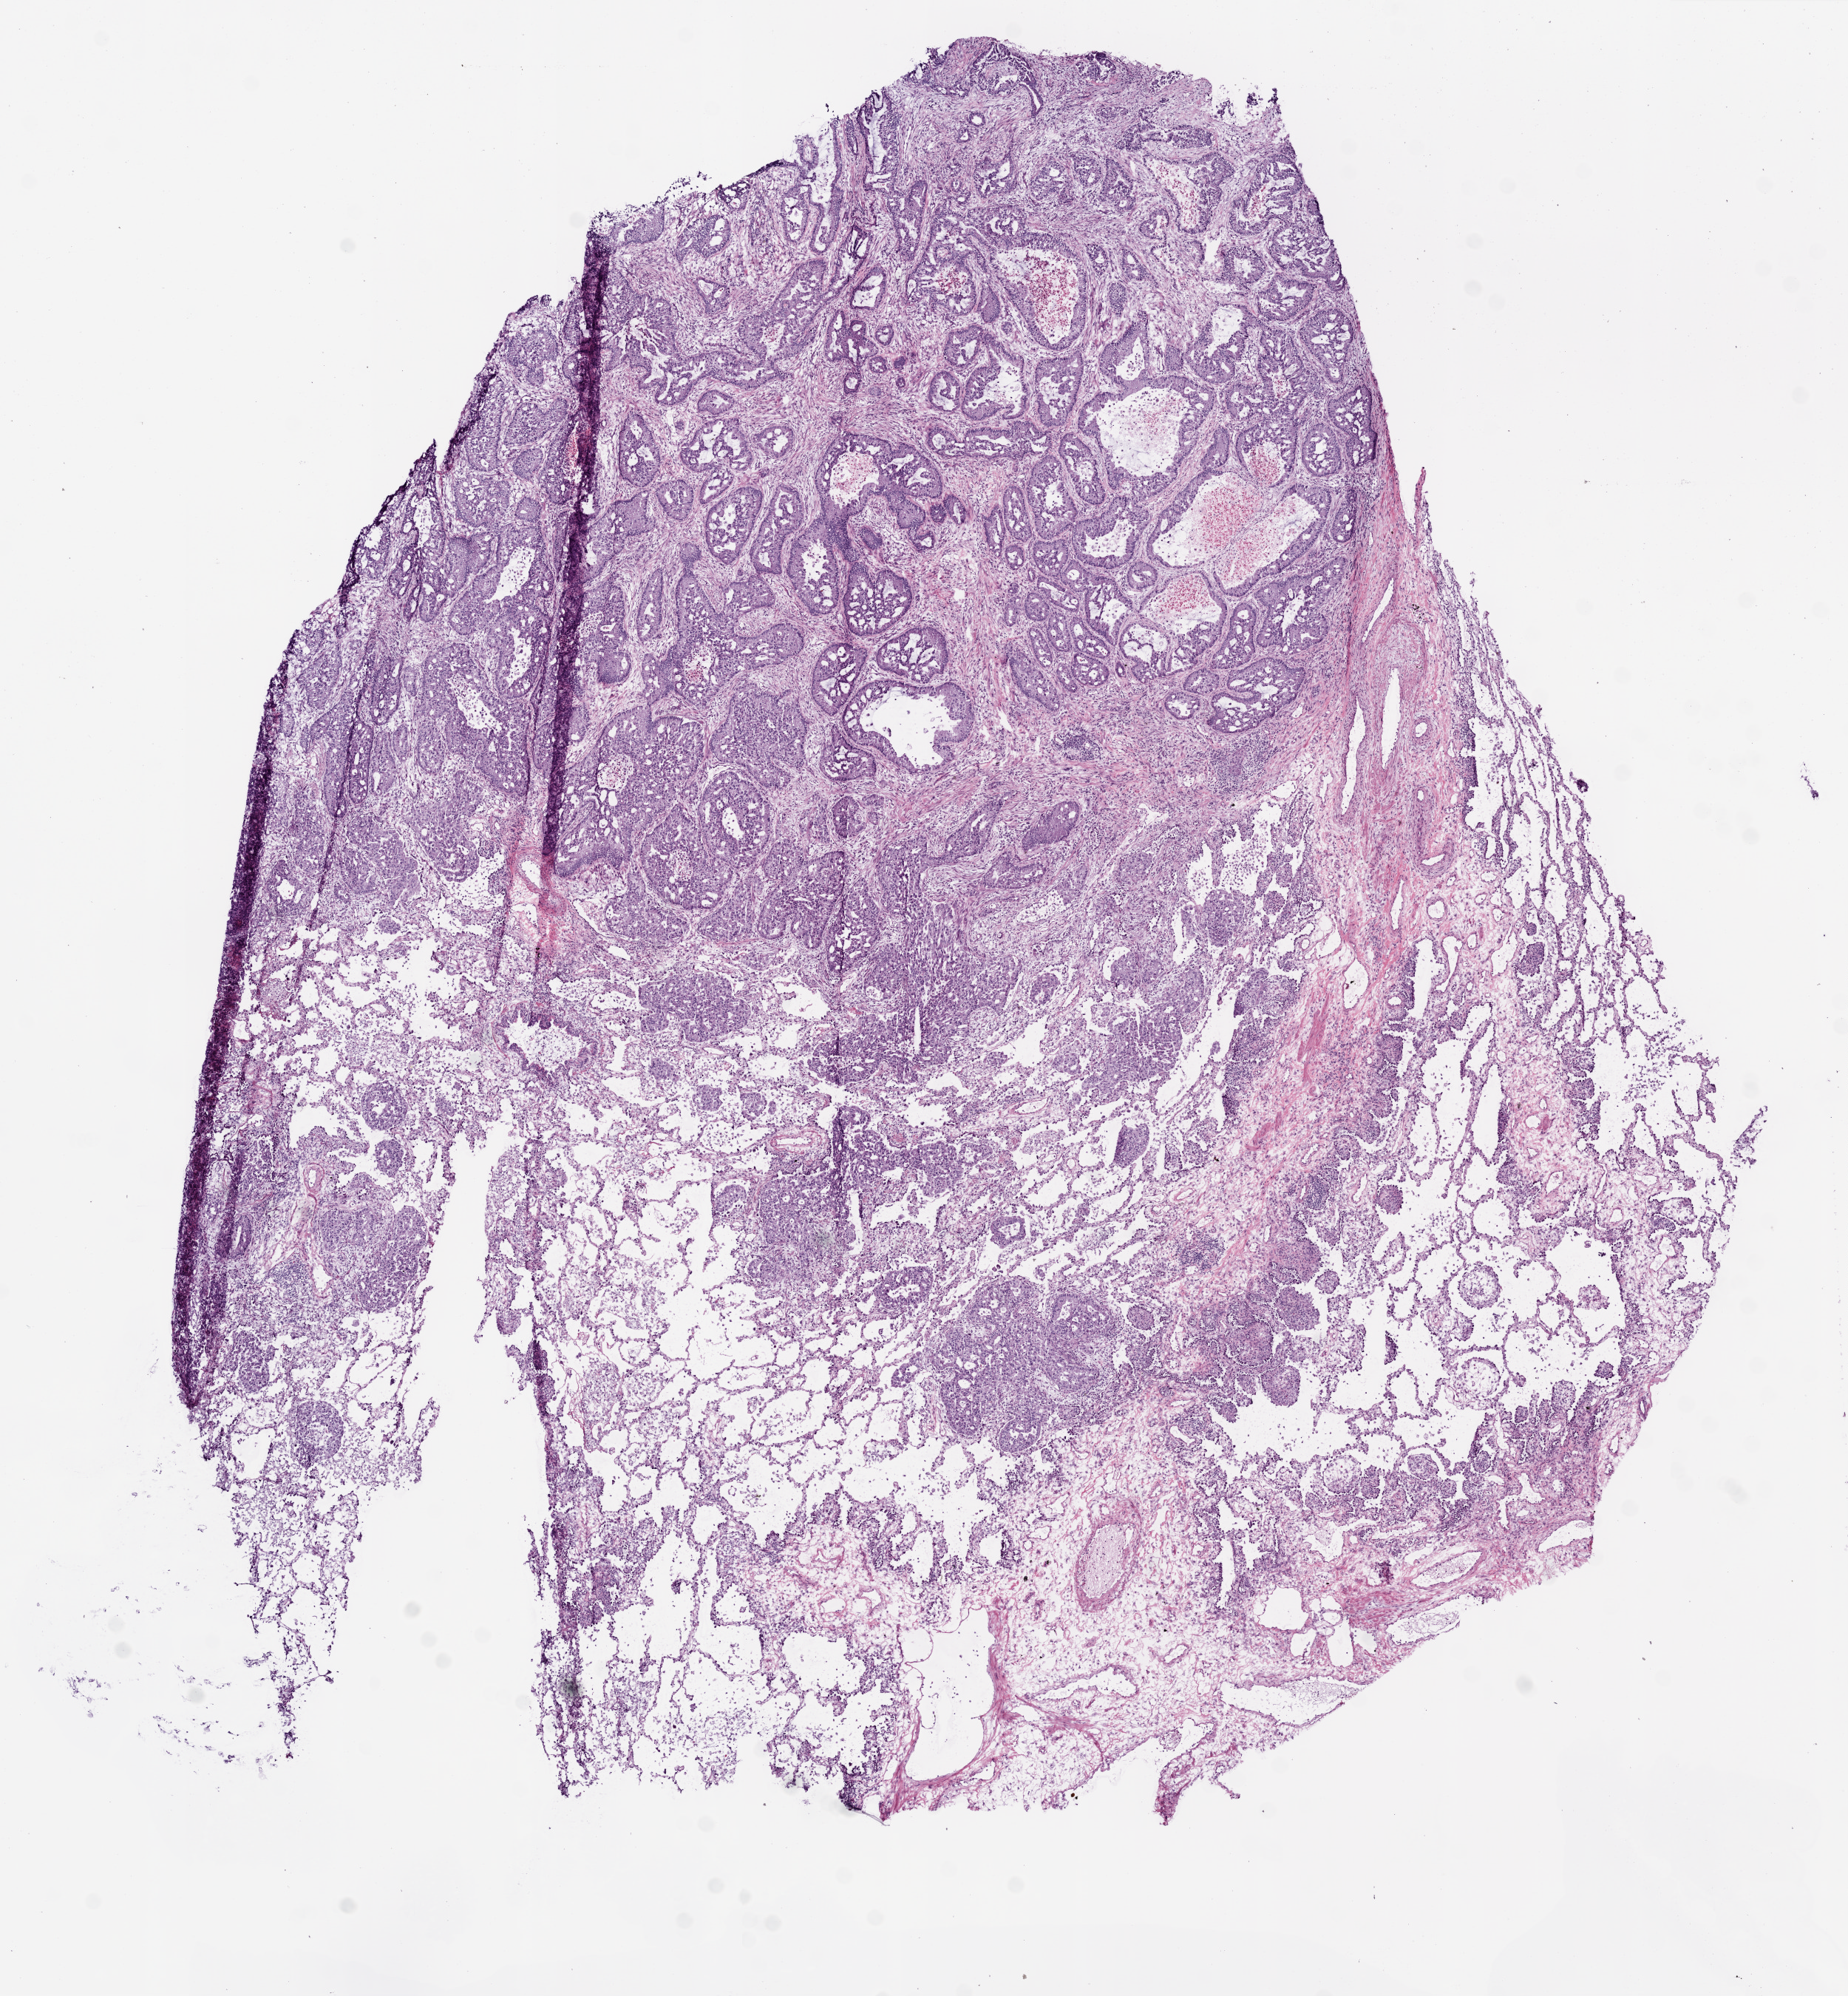
Whole-slide histology image, Hematoxylin and eosin (H&E) stained, whole scanned area (about 10.0 x 10.8 mm) shown as a low-resolution overview. Frozen section from the bottom of the tissue portion. Primary tumour sample from the lung. Male patient; age at initial diagnosis 66 years. Pathologist review of this section (percent, as recorded): tumour cells 70%, tumour nuclei 90%, normal cells 20%, stromal cells 10%, necrosis 0%.
AJCC pathologic stage: IIIA (6th edition). Pathologic diagnosis: Adenocarcinoma, NOS. Laterality: right.